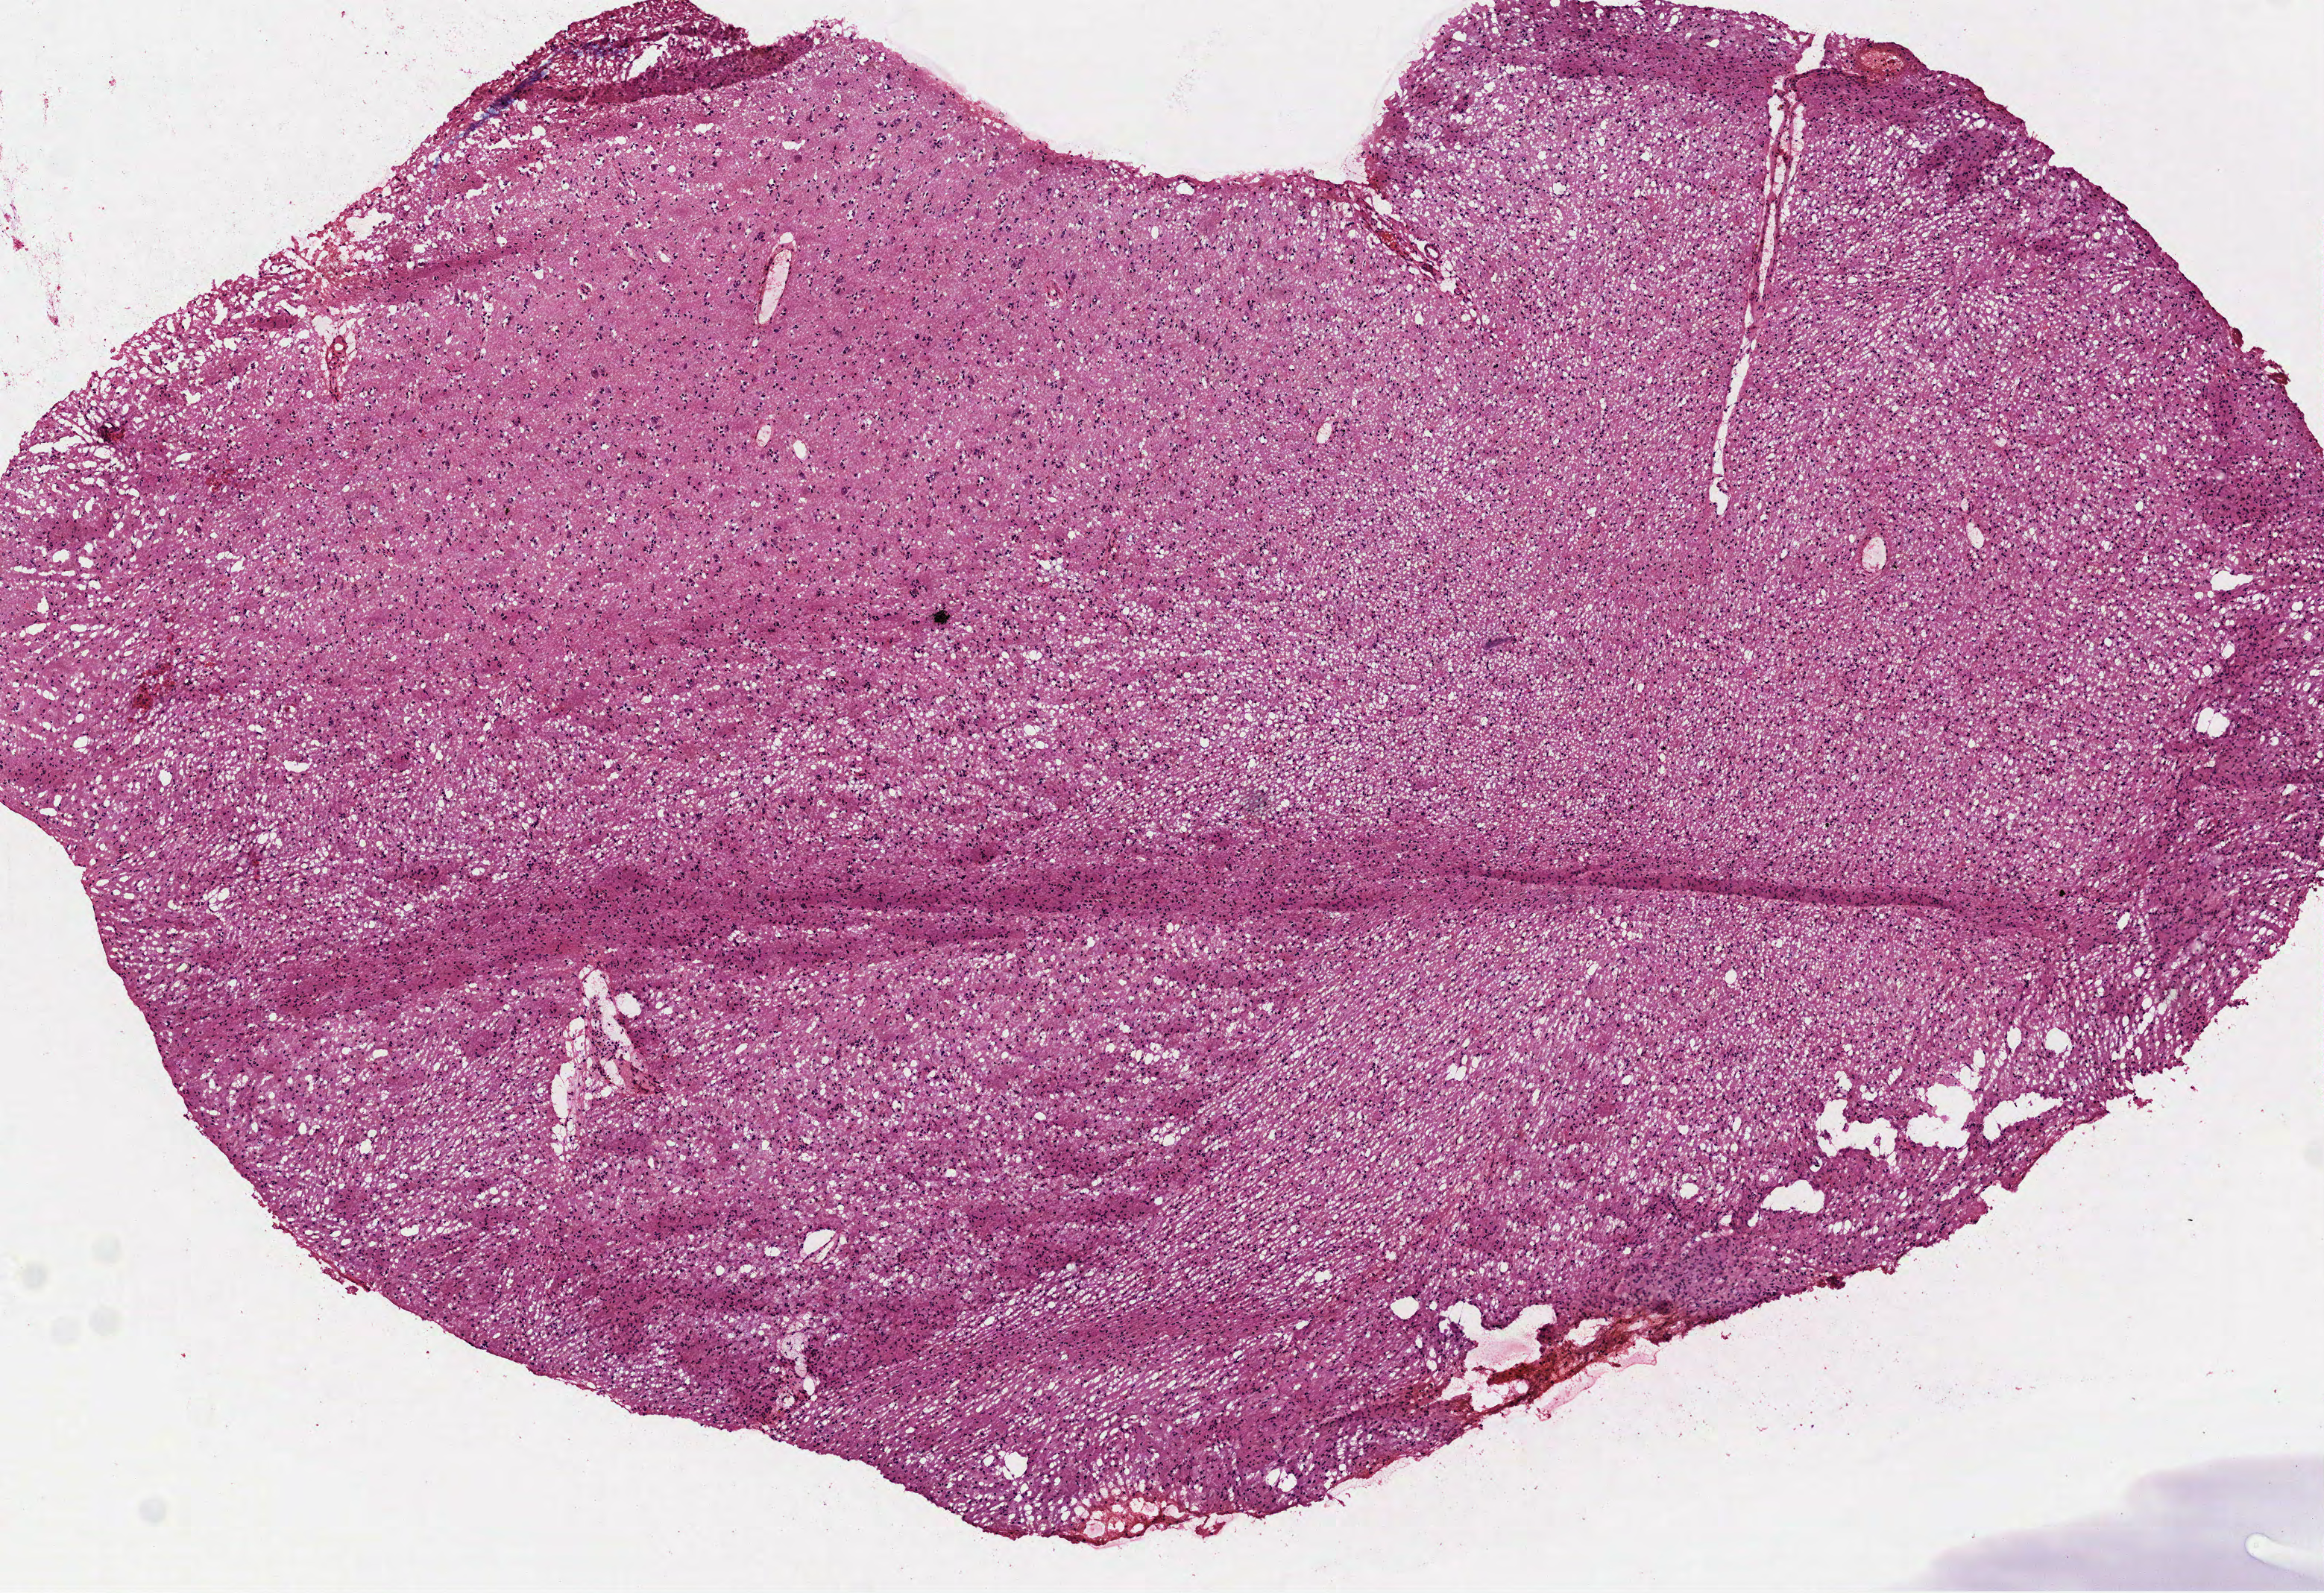
H&E whole-slide image, a low-resolution overview of the entire scanned area, about 6.3 x 4.3 mm (from a 40x scan), frozen section from the top of the tissue portion, brain, primary tumour sample. Male patient; age at initial diagnosis 52 years. Slide review estimates, as recorded: tumour cells 100%, tumour nuclei 65%.
Diagnosis: Mixed glioma (cerebrum).